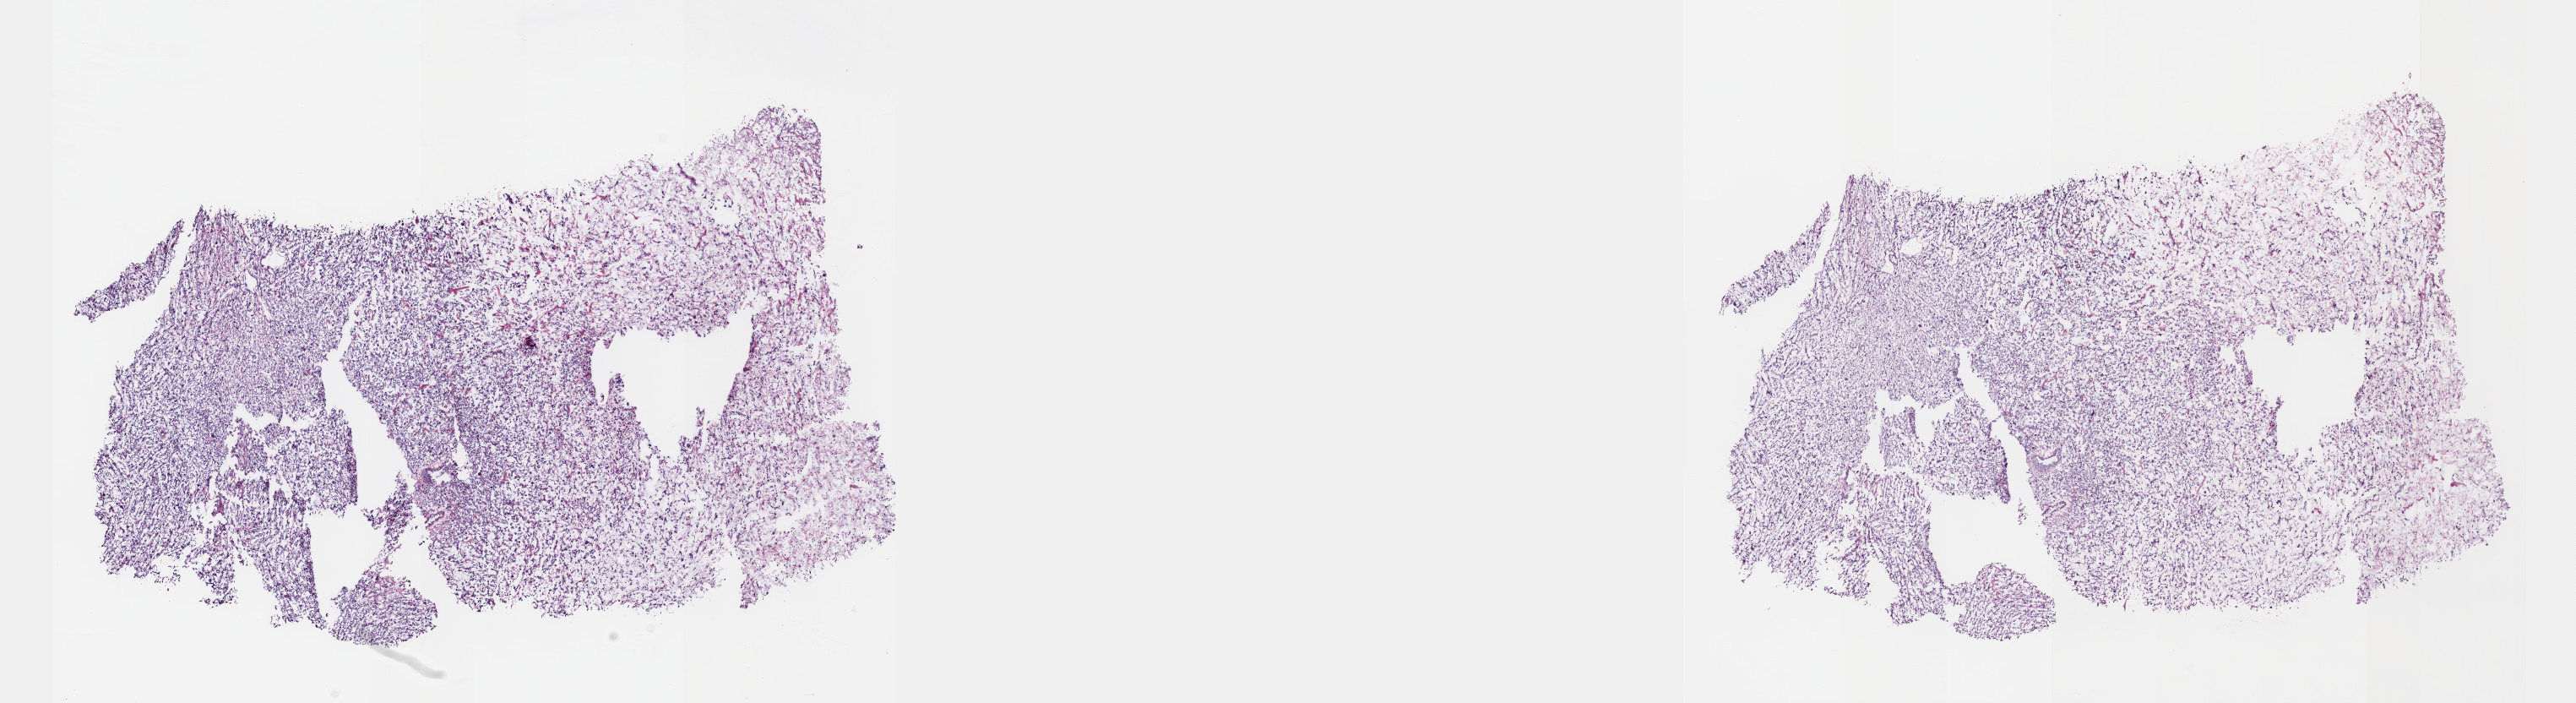
H&E-stained whole-slide image, low-resolution overview of the scanned area, about 24.6 x 6.7 mm. Frozen section from the top of the tissue portion. Primary tumour sample from the connective, subcutaneous and other soft tissues. Male patient. Composition of this section per pathologist review: tumour cells 100%, tumour nuclei 95%, normal cells 0%, stromal cells 0%, necrosis 0%. Inflammatory infiltration, as recorded: lymphocyte infiltration 0%, monocyte infiltration 0%, neutrophil infiltration 0%.
* diagnosis: Dedifferentiated liposarcoma (connective, subcutaneous and other soft tissues of thorax)